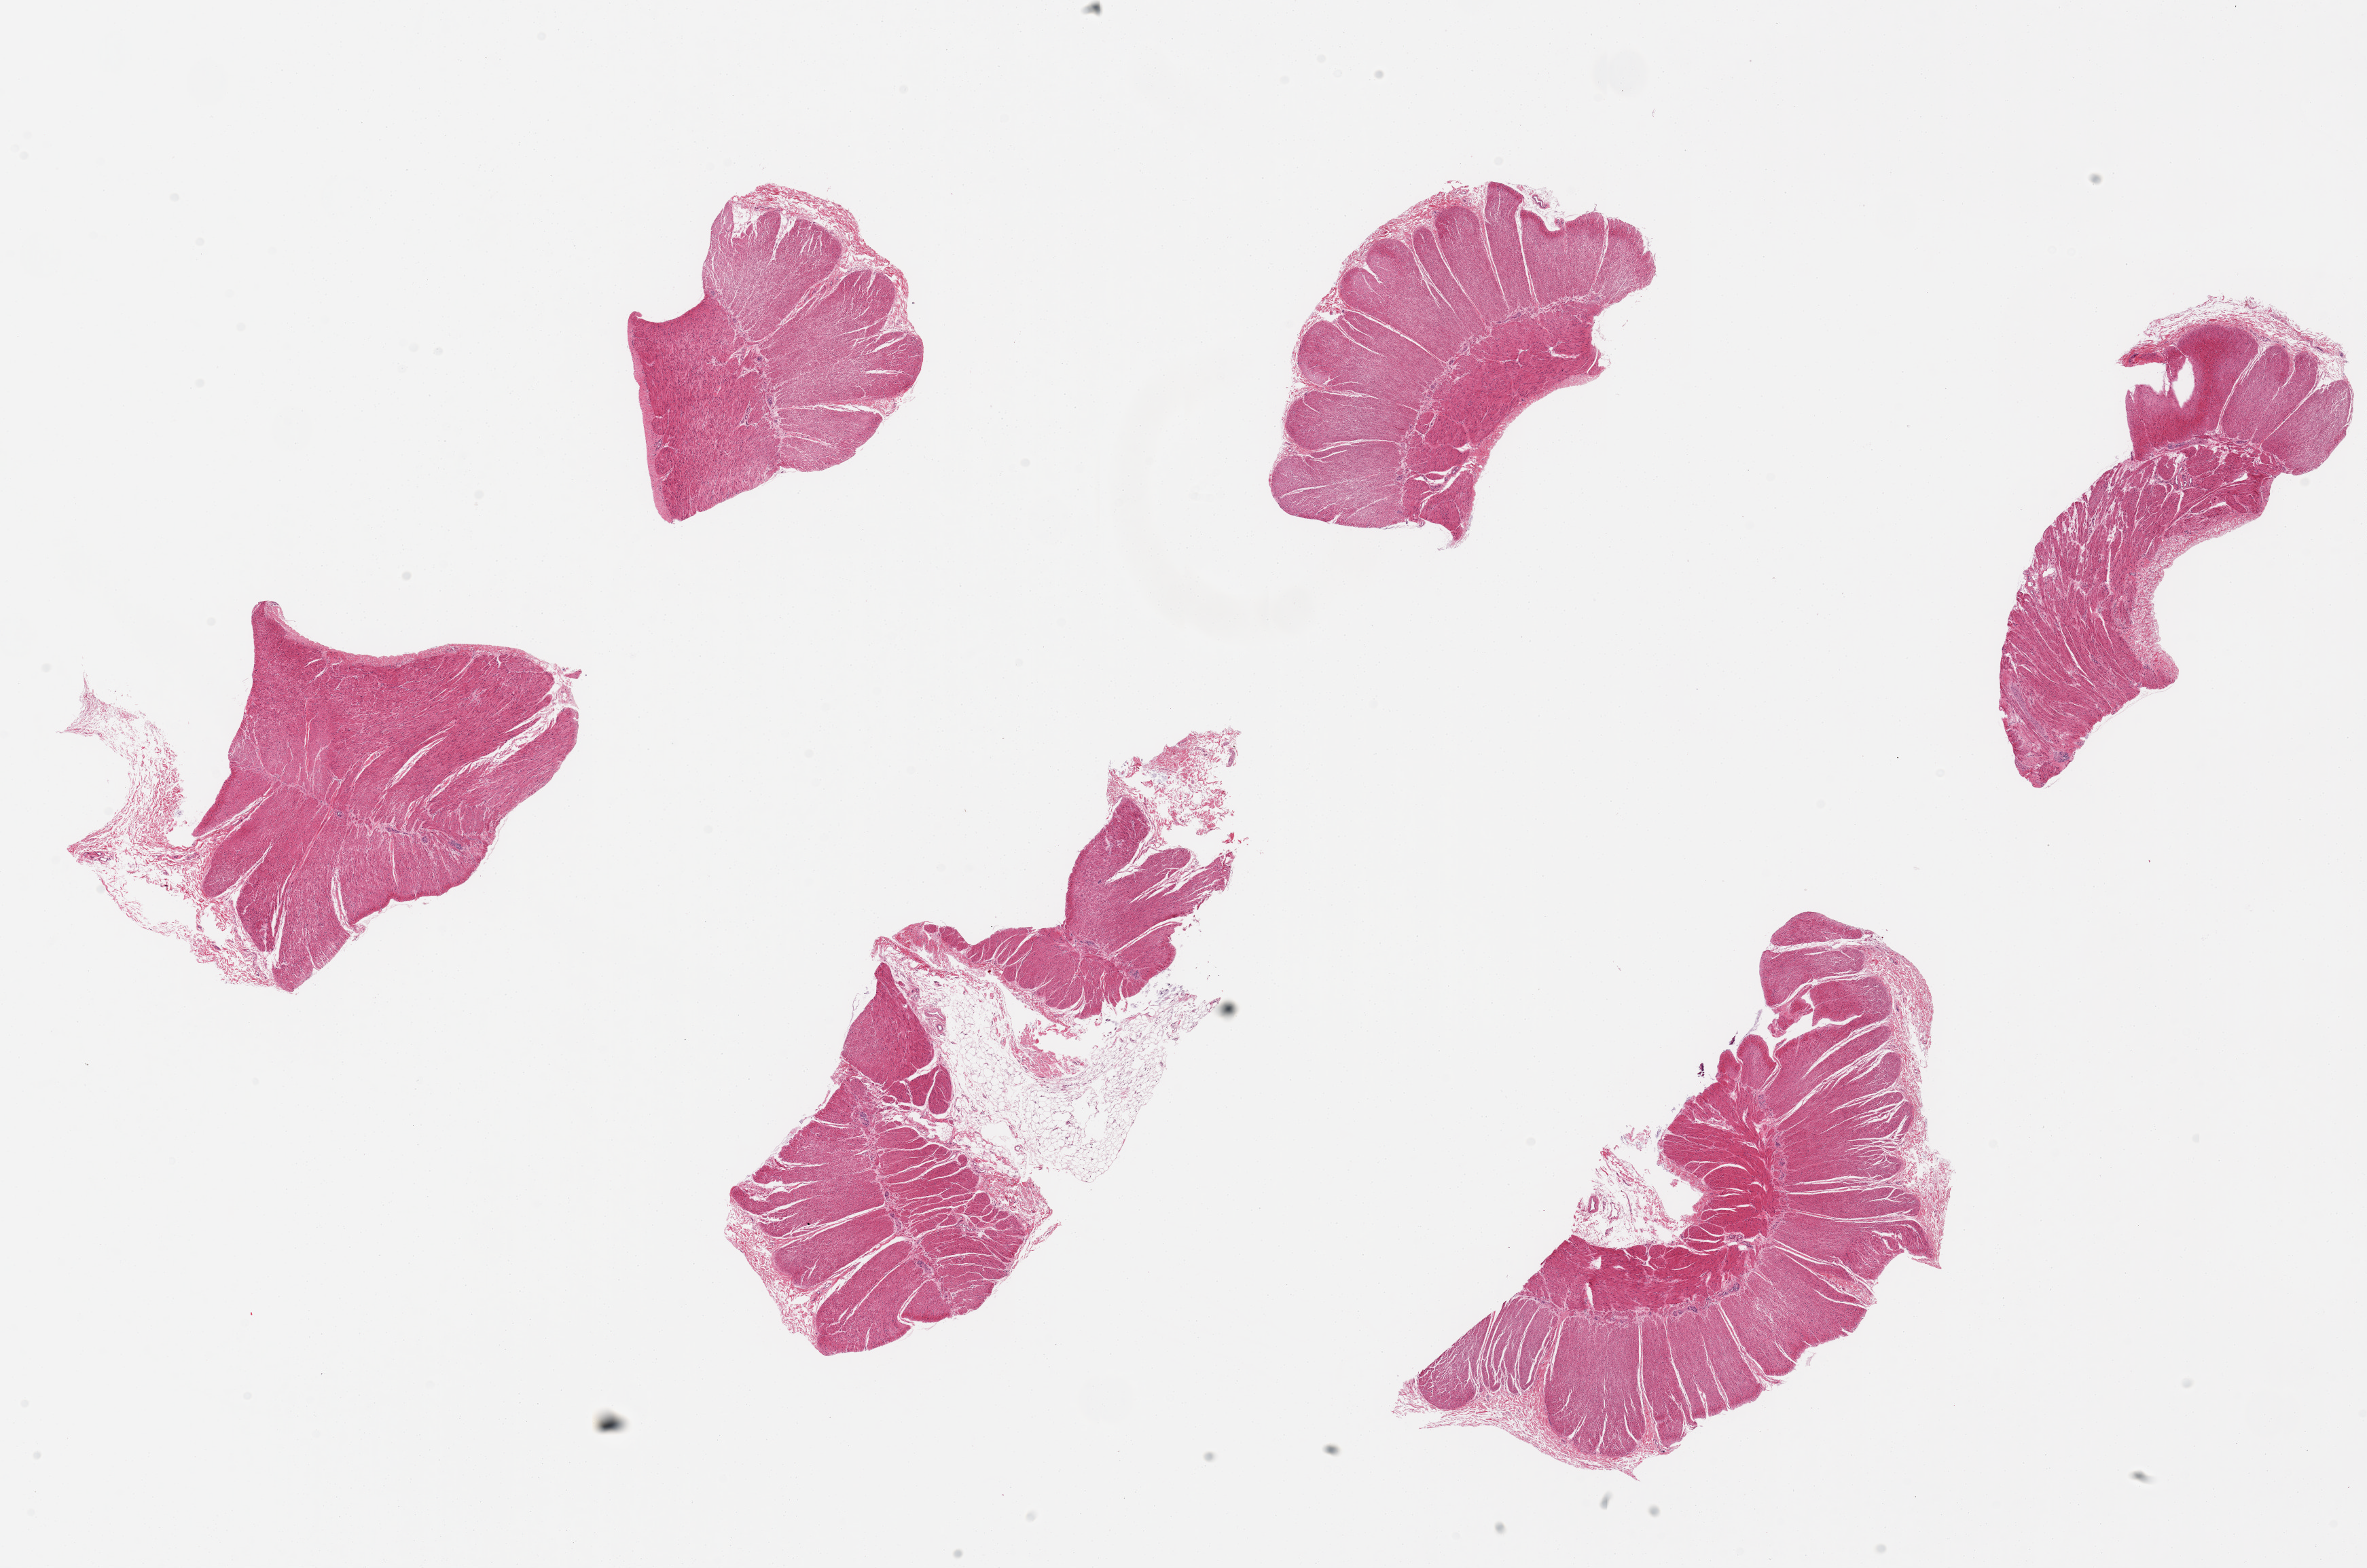
Whole-slide image, haematoxylin and eosin stain, brightfield, low-resolution overview of the scanned area, about 27.6 x 18.3 mm, PAXgene-fixed, paraffin-embedded tissue, sampled site (target tissue): sigmoid colon, tissue donor sample. Donor: female.
Reviewer comment on this tissue sample: 6 pieces, up to 8x4mm; generally all muscularis, a few have adherent fatty nubbins up to ~3mm thick.